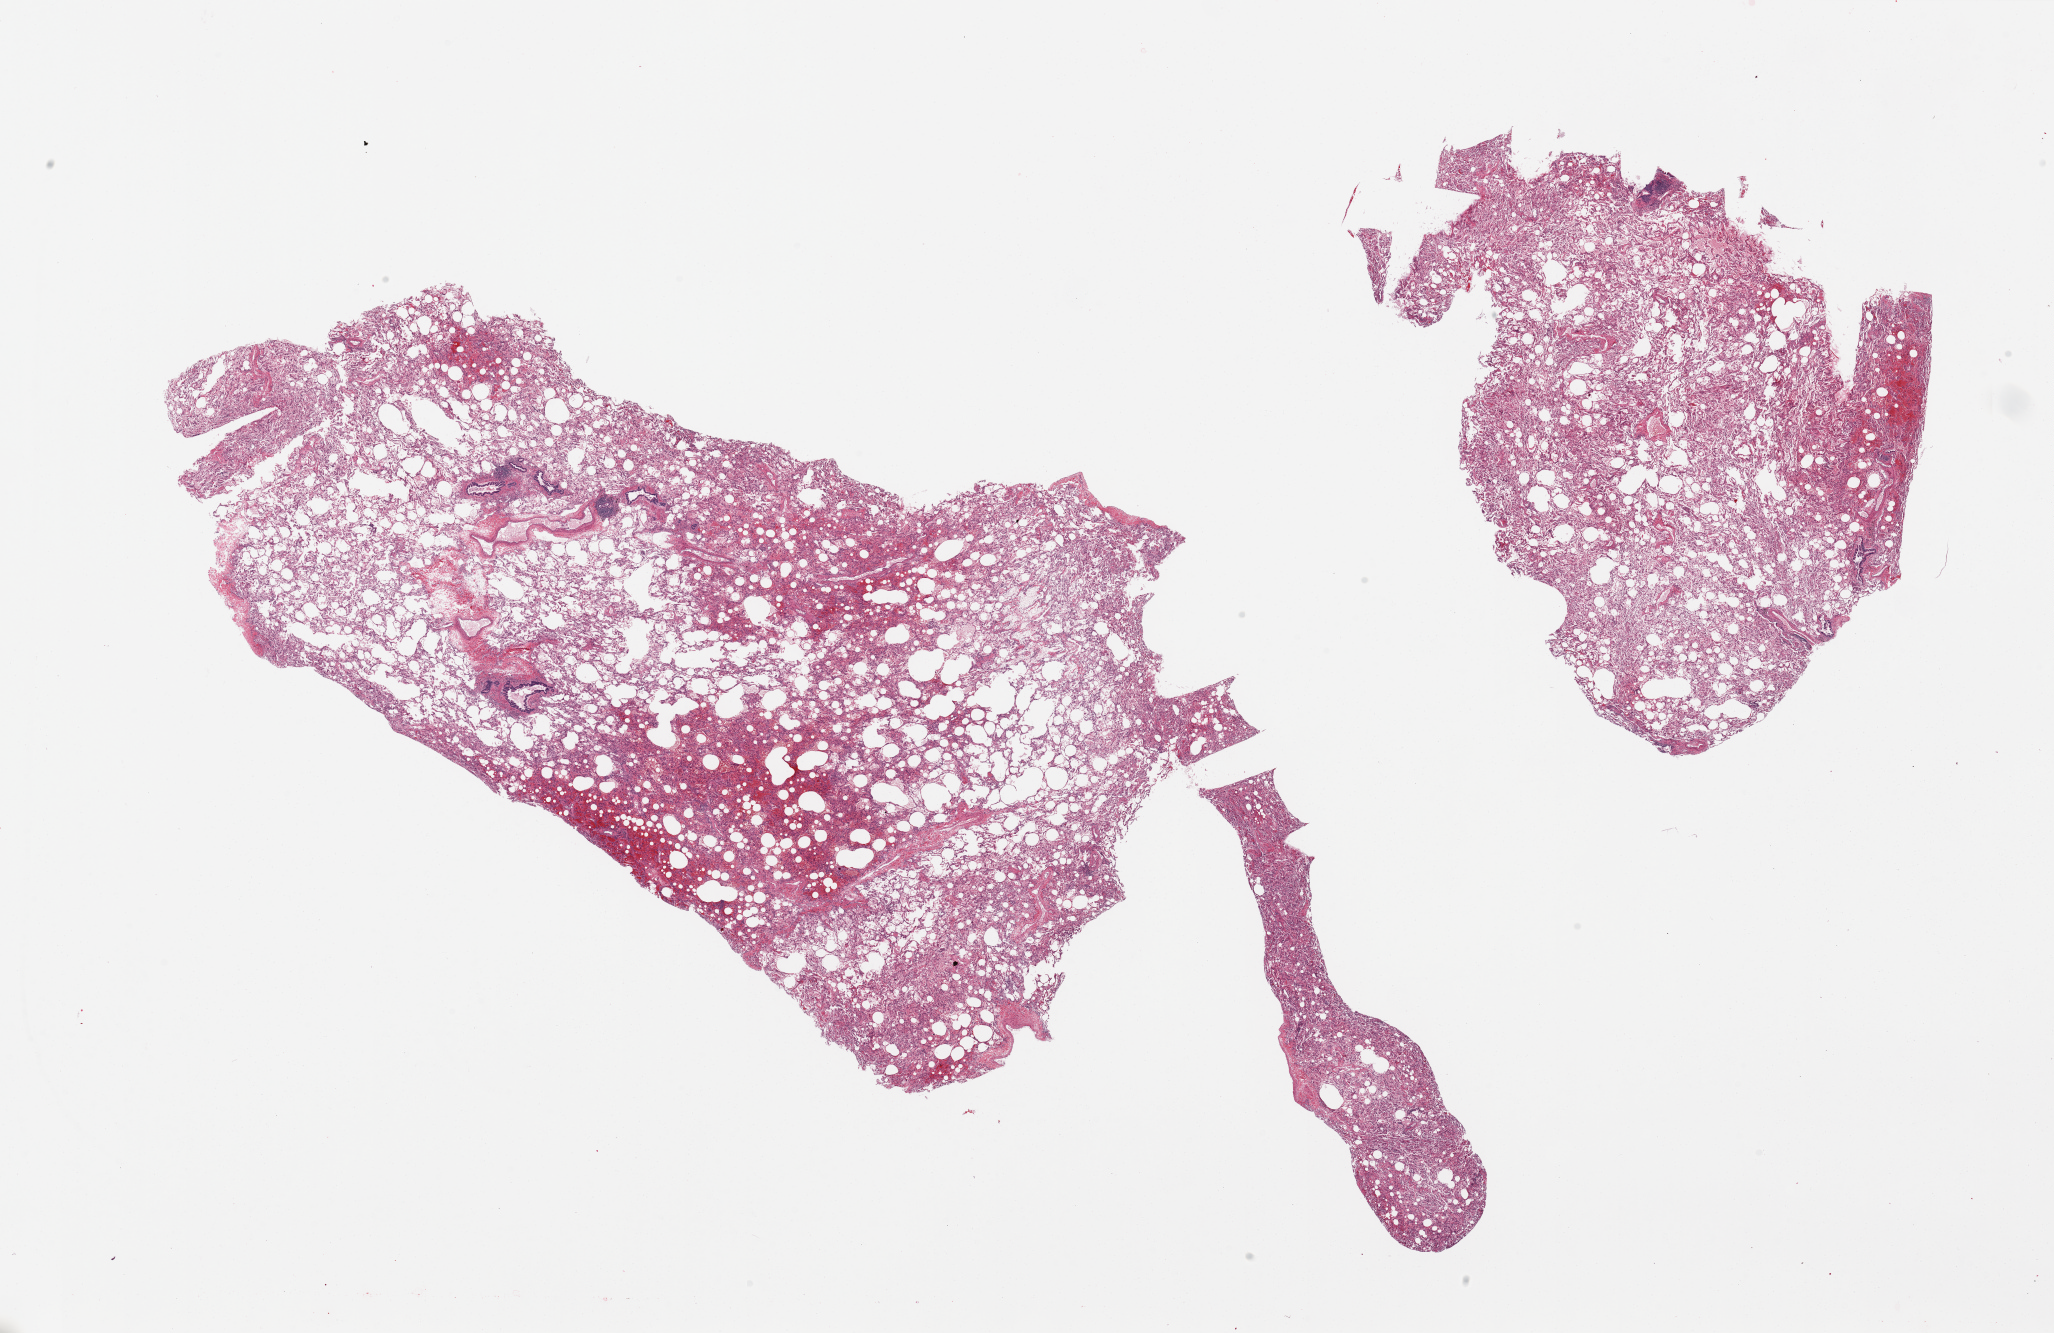
Digitized haematoxylin and eosin-stained section — a low-resolution overview of the entire scanned area, about 32.5 x 21.1 mm. PAXgene-fixed, paraffin-embedded tissue. Sampled site (target tissue): lung. Tissue donor sample. Donor: male.
Review note (as recorded): 2 pieces, well preserved, broncial mucosa, patchy congestion/hemorrhagic pneumonitis.